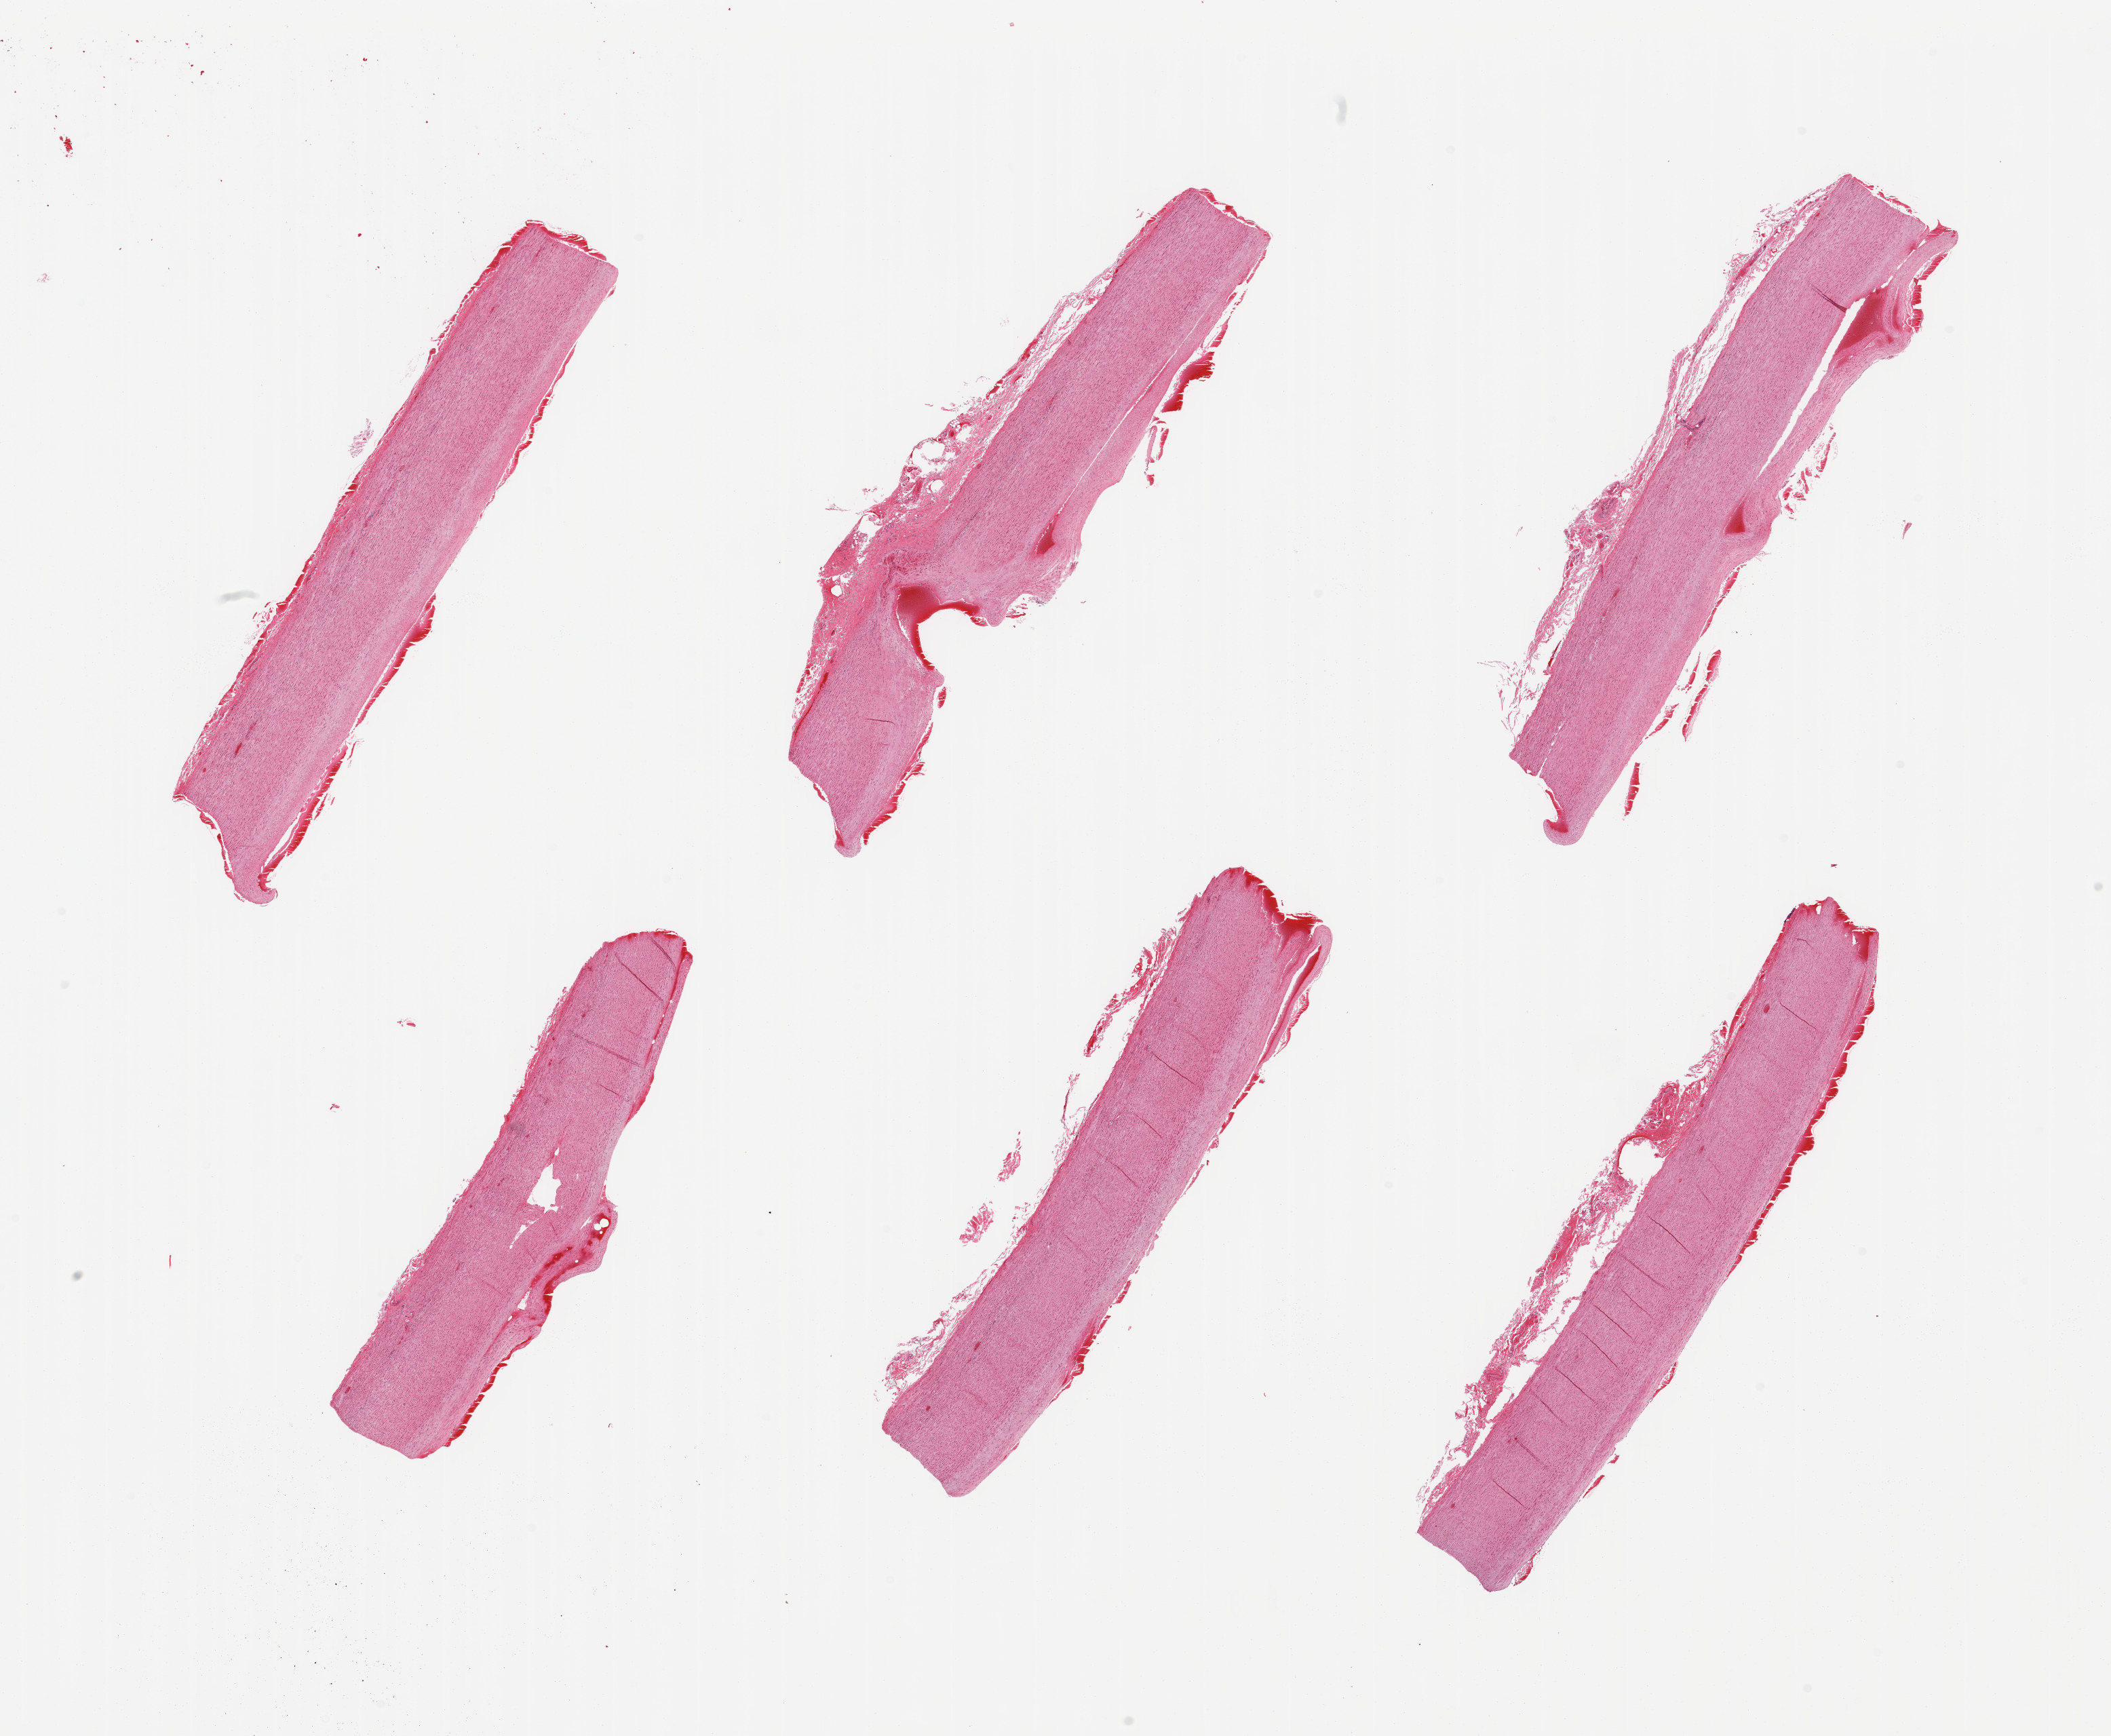
Whole-slide image, H&E stain, brightfield, a low-resolution overview of the entire scanned area, about 24.6 x 20.2 mm (from a 20x scan); PAXgene-fixed, paraffin-embedded tissue; section of aorta (target tissue); tissue donor sample. Male donor.
Pathologist's review note for this sample: 6 pieces; dissecting atherosclerotic plaque; up to 0.6mm attached adventitia.